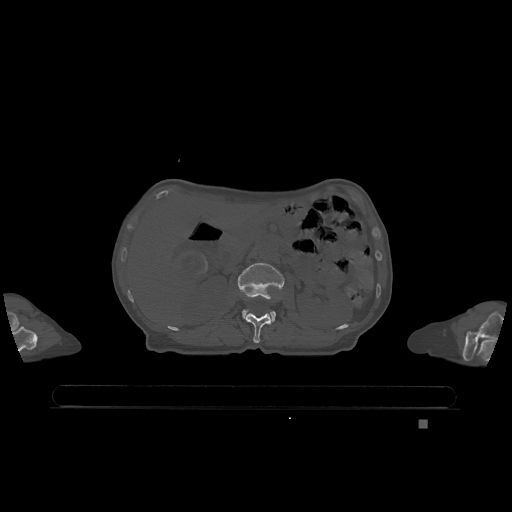
CT including the spine, one axial slice. Position 450 of 1317 along the scan axis. Bone window (W 1800 / L 400 HU). 512 × 512 image matrix, field of view 500 × 500 mm. Female patient, age 74 years. Case-level facts recorded for this patient, not image findings: primary cancer: lung; vertebrae with lytic lesions (as recorded): T1, T4, T5, T6, L4, L5.
Outlined on this slice (semi-automatic segmentation, software-assisted and operator-edited):
- L1 vertebra: box from (x=245, y=313) to (x=271, y=343) px
- L2 vertebra: (x=238, y=263)–(x=285, y=323)